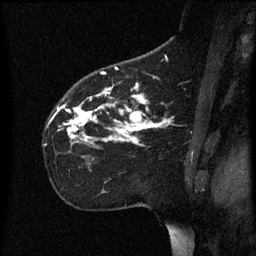
Breast MRI (dynamic contrast-enhanced), one sagittal slice. Position 40 of 60 along the scan axis. Dynamic contrast-enhanced series, image 2 of 3 at this slice position (ordered by acquisition). 1.5 T. TE 4.2 ms, TR 8.4 ms. 2.2 mm slice thickness. 256 × 256 image matrix. Patient: female, 35 years. Case-level facts recorded for this patient, not image findings: setting: breast cancer imaged before/during neoadjuvant chemotherapy; receptor status: HER2-positive.
Outlined on this slice (semi-automatically segmented with operator editing):
- analysis volume of interest (the breast-tissue region the enhancement analysis was run in; not a lesion): bounding box <45,78,173,163> (left, top, right, bottom; pixels)
- tumour enhancement mask (voxels above the 70 % enhancement threshold inside the analysis volume of interest): <62,84,171,145>